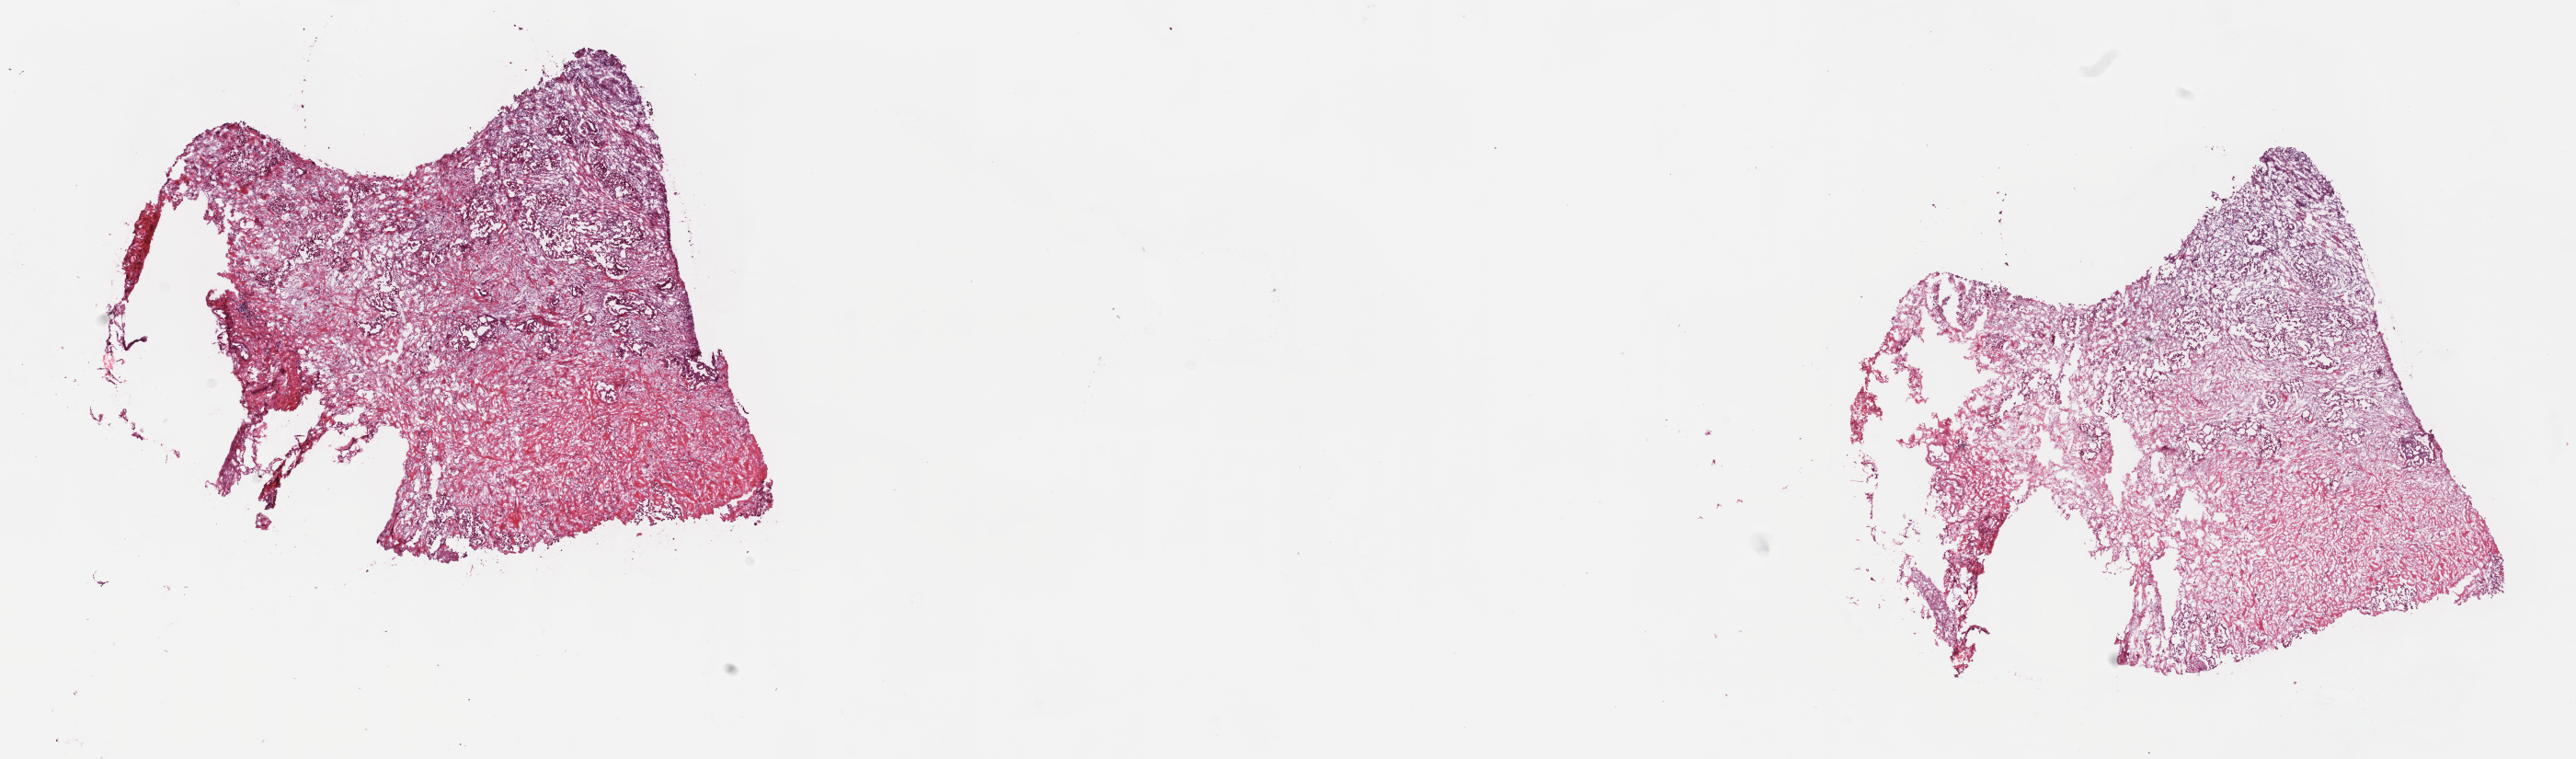
Digitized H&E tissue section (whole slide), a low-resolution overview of the entire scanned area, about 22.7 x 6.7 mm (slide scanned at 40x). Frozen section. Bile duct, primary tumour sample. Male patient; age at initial diagnosis 74 years.
Pathologic diagnosis: Cholangiocarcinoma (intrahepatic bile duct).